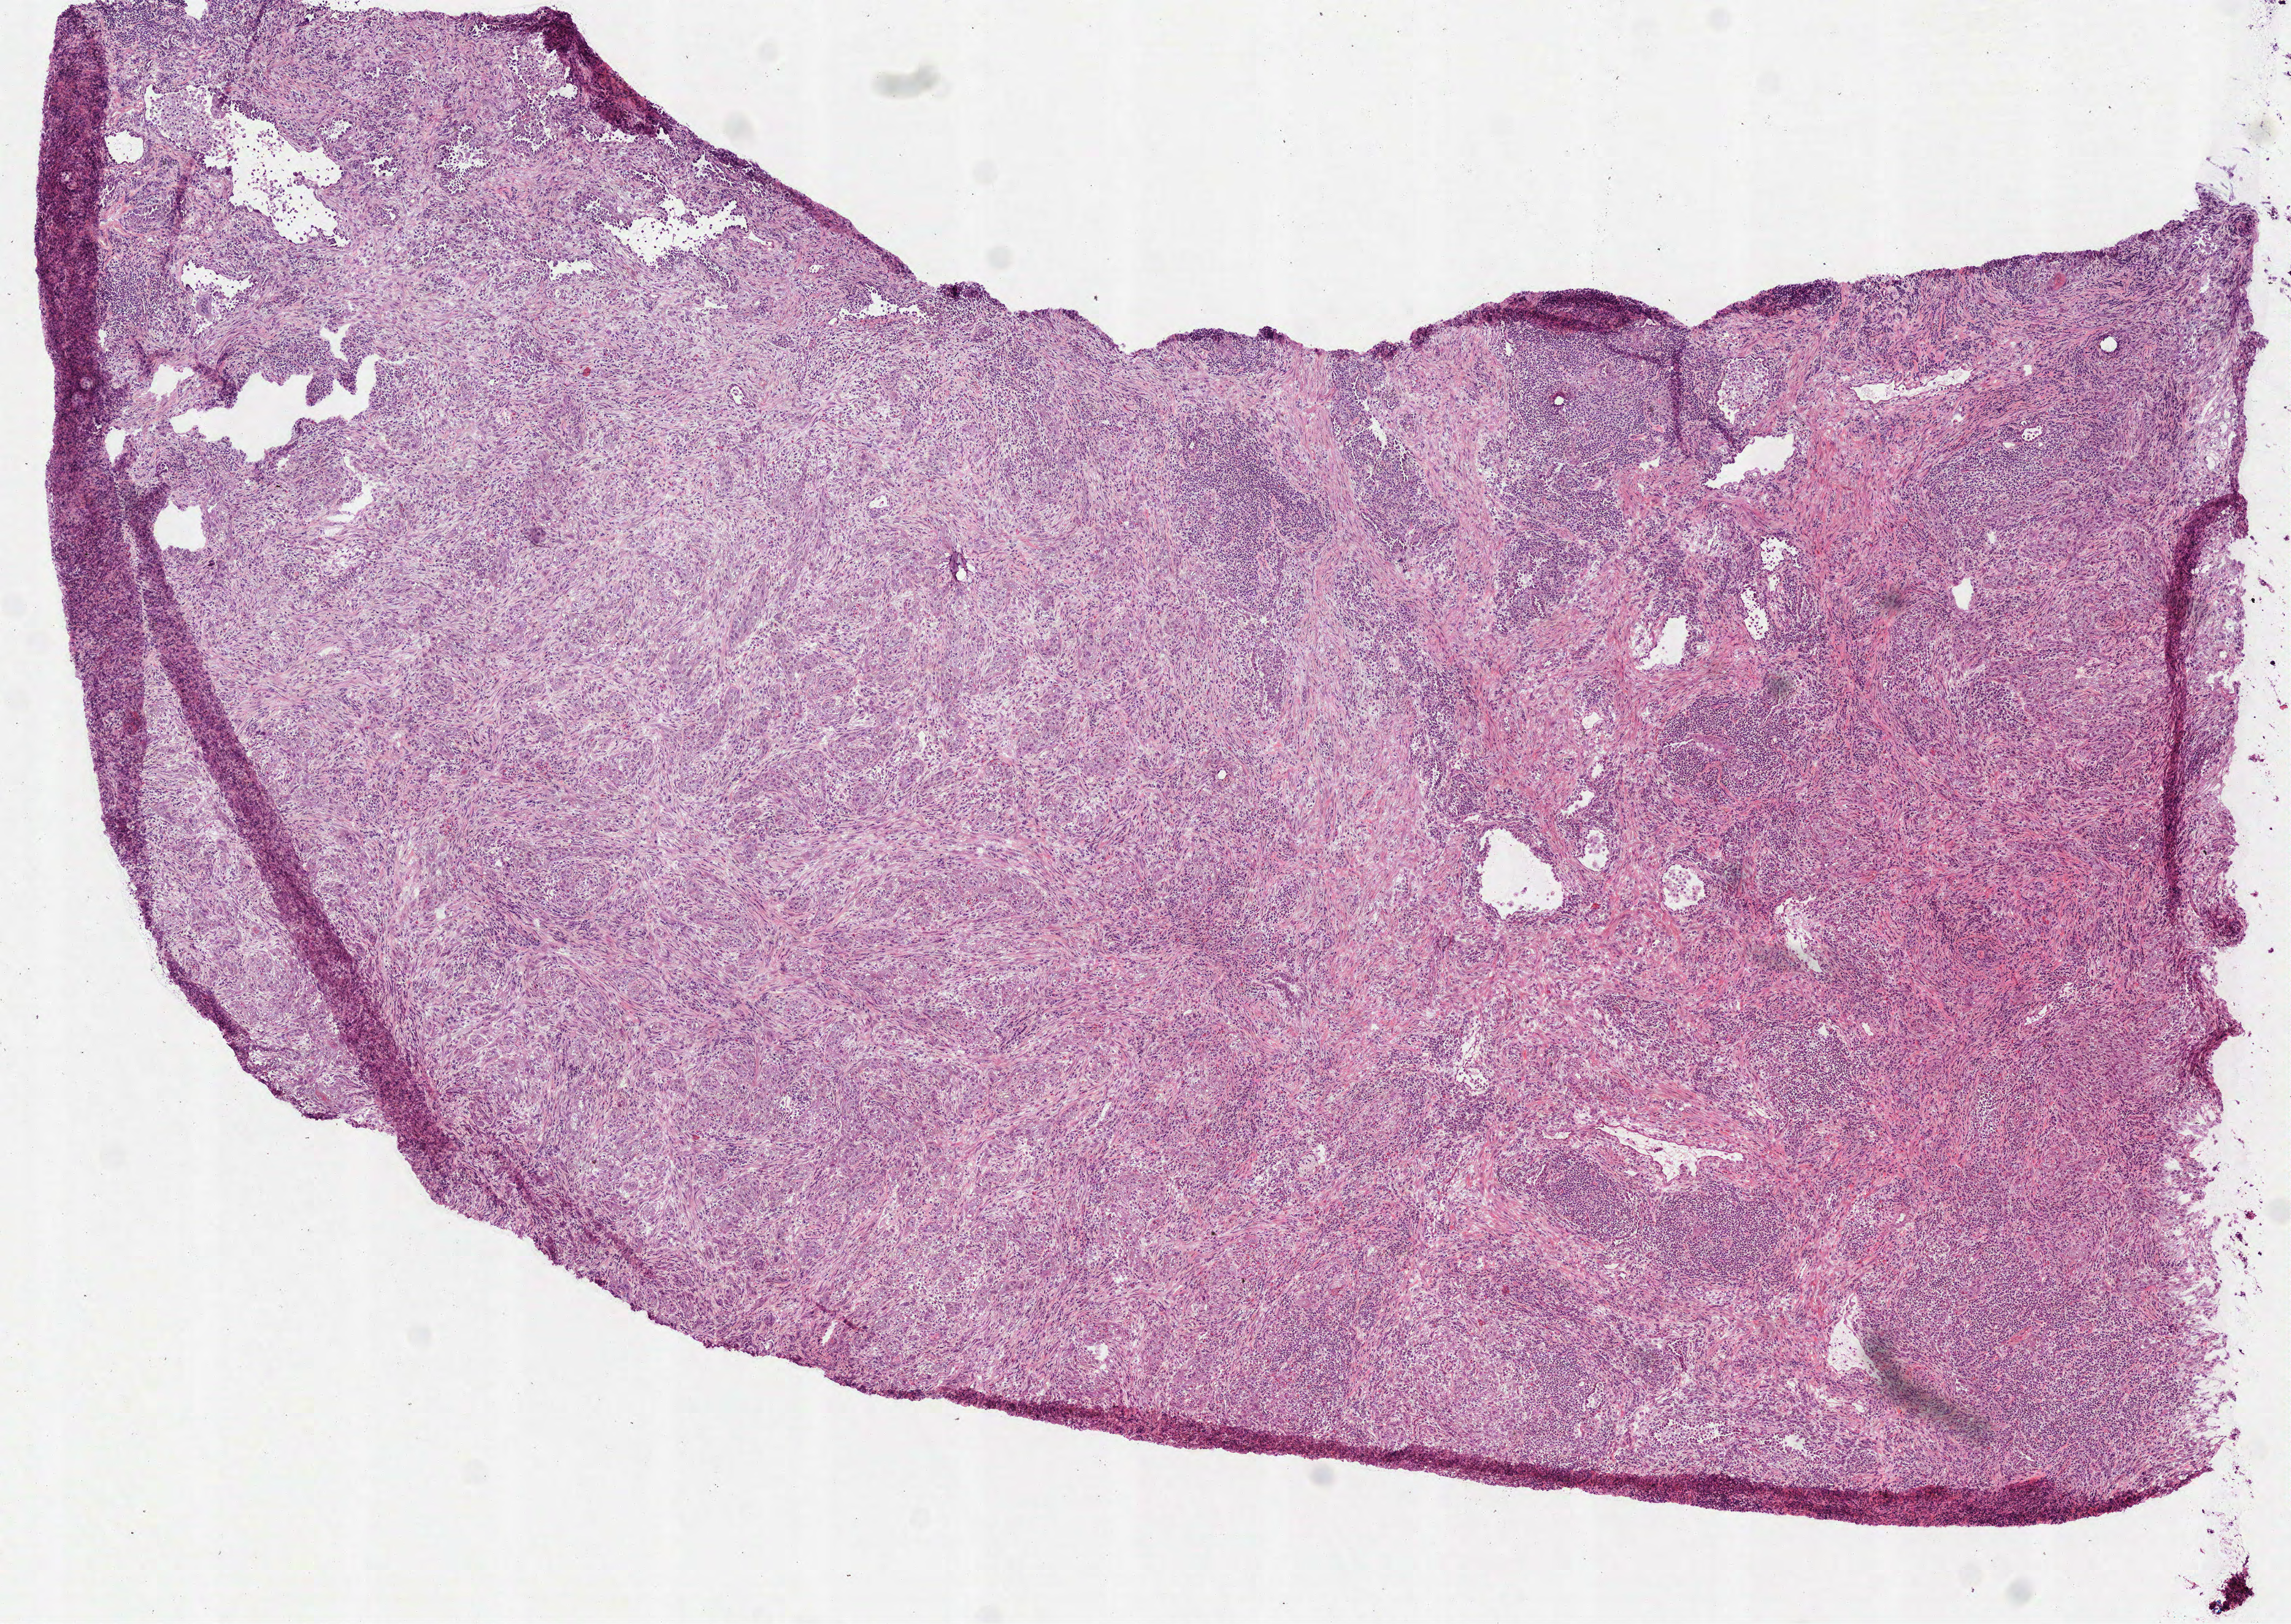
Digitized H&E tissue section (whole slide), whole scanned area (about 7.5 x 5.3 mm, from a 40x scan) shown as a low-resolution overview. Frozen section. Sample: primary tumour, lung. Patient: female, age at initial diagnosis 69 years. Pathologist review of this section (percent, as recorded): tumour cells 90%, tumour nuclei 65%, normal cells 10%, stromal cells 0%, necrosis 0%. Infiltration values recorded for this section: lymphocyte infiltration 25%, monocyte infiltration 2%, neutrophil infiltration 5%.
AJCC pathologic stage: IIB. Diagnosis: Squamous cell carcinoma, NOS (lower lobe, lung).